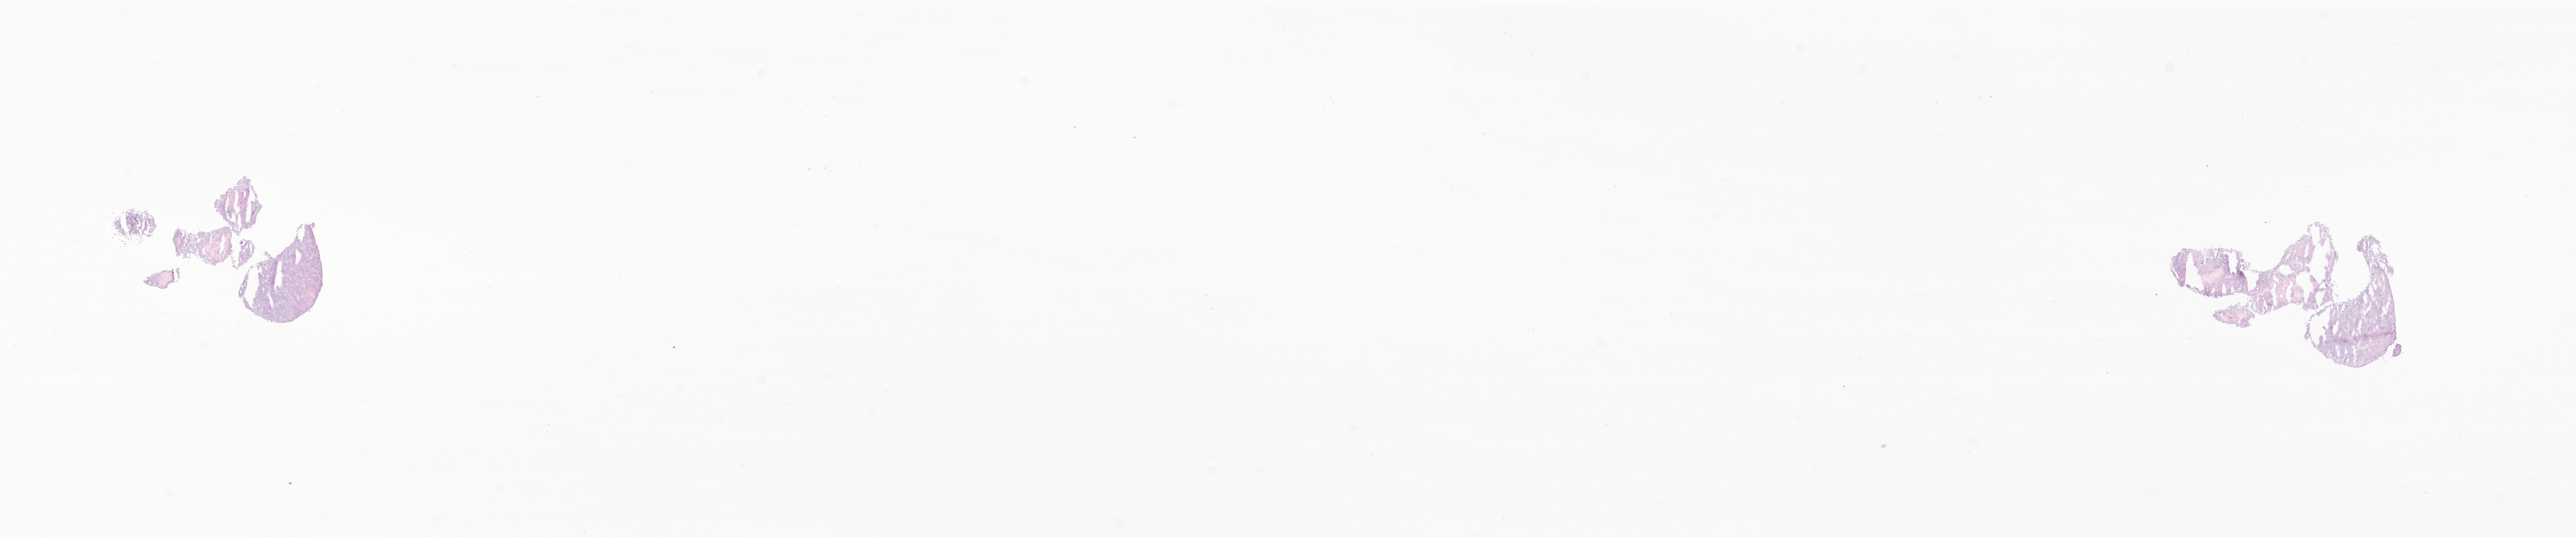
H&E whole-slide image of tumor tissue from the brain — whole scanned area (about 27.5 x 5.7 mm) shown as a low-resolution overview. Frozen section (OCT-embedded). Patient: male, age 217 months (18 years 1 month).
Diagnosis: Ganglioglioma, NOS.